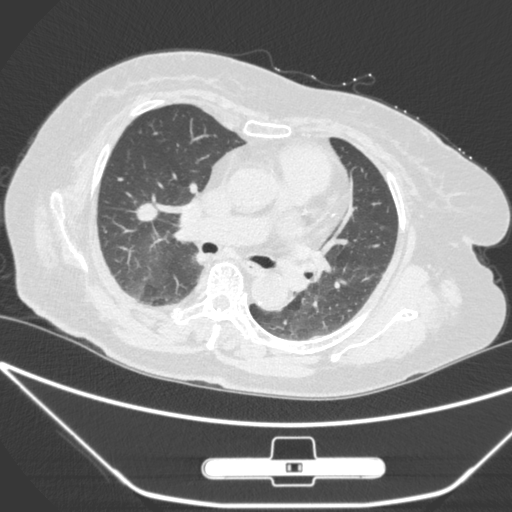
Chest CT, one axial slice; slice 156 of 245 in the series (ordered by position); lung window (W 1500 / L -600 HU); 512 × 512 image matrix, field of view 365 × 365 mm. Patient: female, 65 years. From the clinical record (not read from this slice): clinical TNM (as recorded): T1c N0 M0.
Structures marked on this image (bounding box drawn by a radiologist):
- lung tumour (recorded histology: adenocarcinoma): bounding box [x1, y1, x2, y2] px = [127, 189, 169, 228]